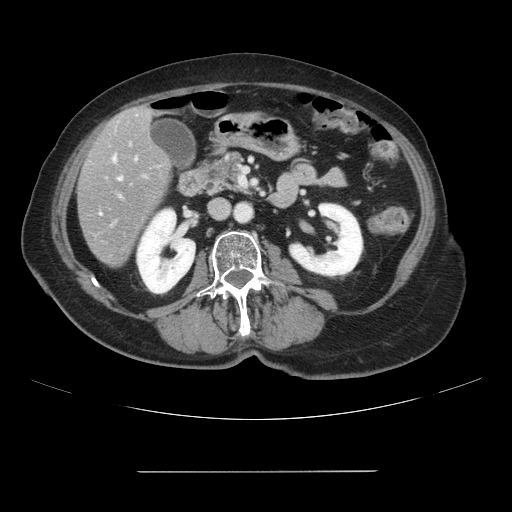
Contrast-enhanced abdominal CT, one axial slice. Position 27 of 111 along the scan axis. Intravenous contrast given. Soft-tissue window (W 400 / L 40 HU). 2.5 mm slice thickness. 512 × 512 image matrix, field of view 400 × 400 mm. Female patient, age 74 years. Case-level facts recorded for this patient, not image findings: diagnosis: colorectal cancer liver metastases, imaged before liver resection; multiple liver metastases: yes; largest metastasis: 1.1 cm; chemotherapy before resection: yes.
Outlined on this slice (manually delineated by an expert):
- hepatic veins: bounding box [x1, y1, x2, y2] px = [114, 158, 121, 180]
- liver: [78, 107, 172, 267]
- planned liver remnant (the part of the liver to remain after resection): [143, 109, 153, 118]